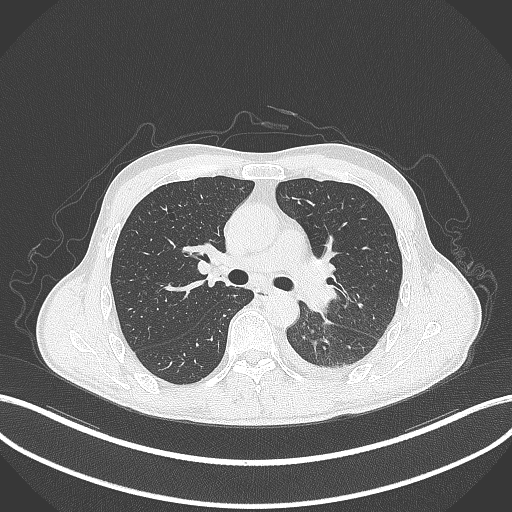
Chest CT, one axial slice. Position 202 of 295 along the scan axis. Reconstruction kernel B70f. Lung window (W 1500 / L -600 HU). 1 mm slice thickness. 512 × 512 image matrix, field of view 400 × 400 mm. Male patient, age 47 years. Case-level facts recorded for this patient, not image findings: clinical TNM (as recorded): T3 N1 M1c.
Outlined on this slice (bounding box drawn by a radiologist):
- lung tumour (recorded histology: small cell carcinoma): box from (x=294, y=280) to (x=339, y=315) px